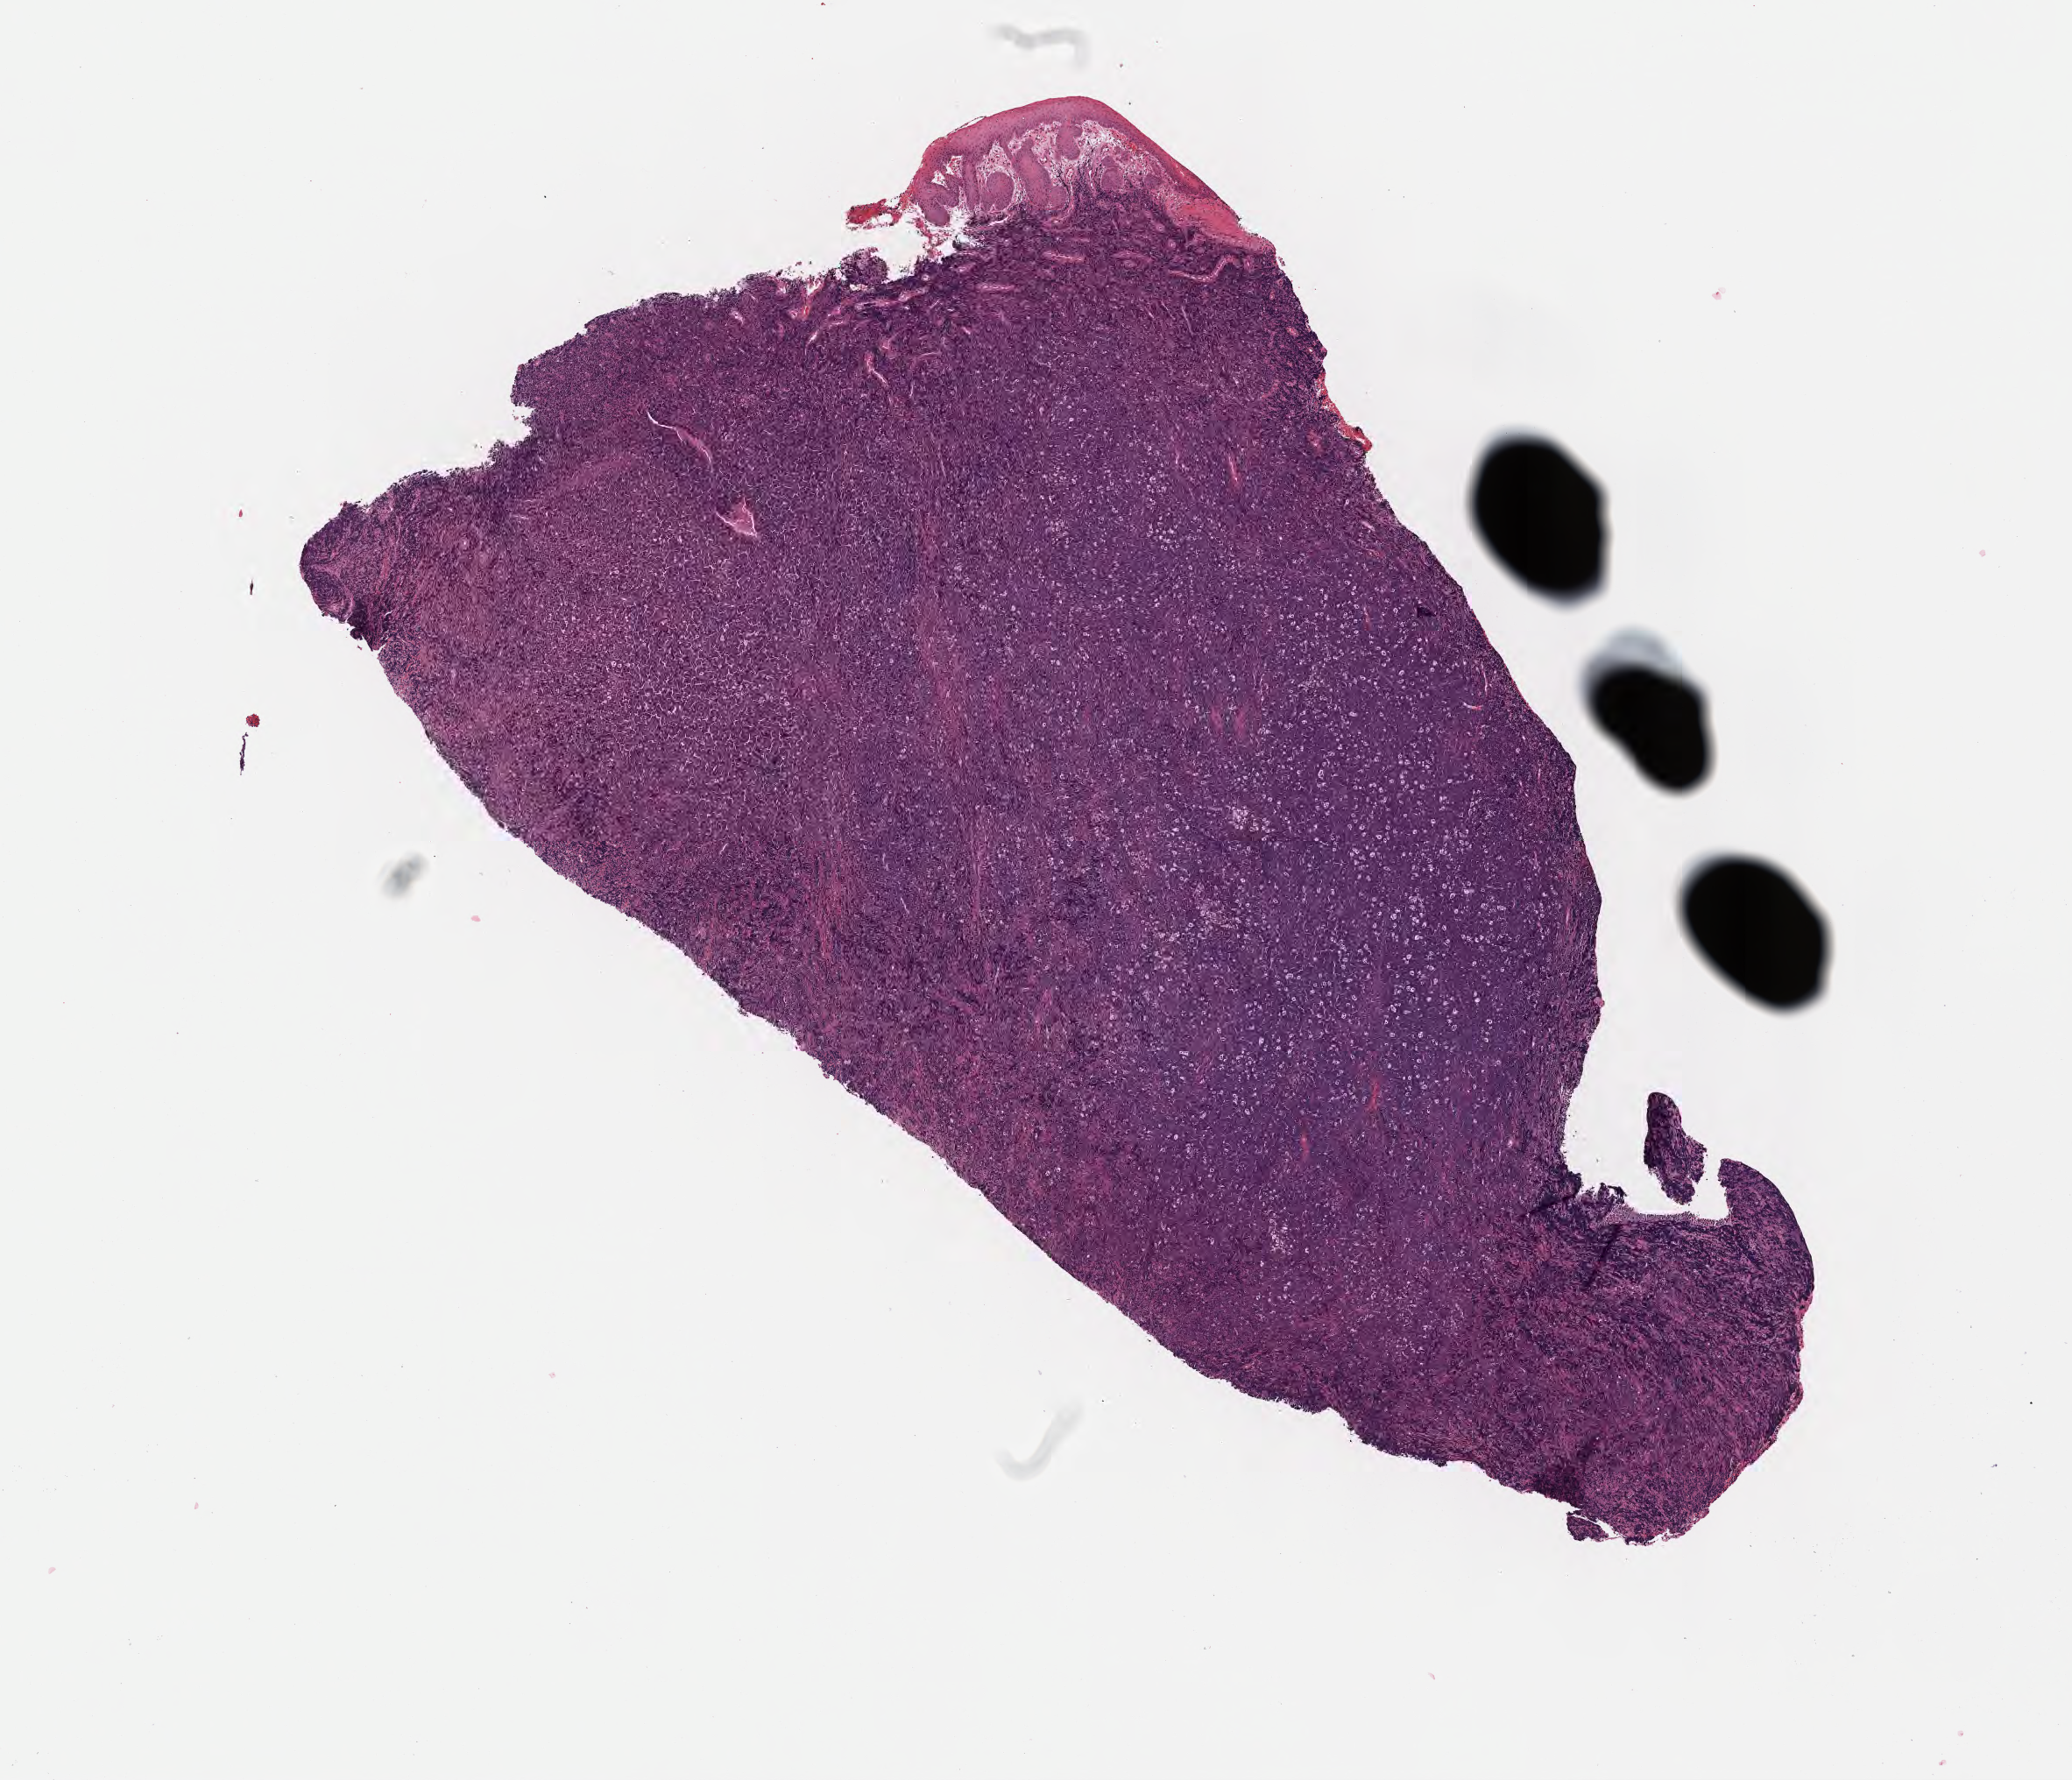
Whole-slide image, H&E stain, shown as a low-resolution overview of the whole scanned area (about 9.6 x 8.2 mm); specimen: tumor tissue; site: mandible. Patient: male, age at initial diagnosis 8 years.
Diagnosis: Burkitt lymphoma, NOS.